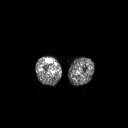
FDG PET of an extremity soft-tissue mass (from a PET/CT study), one axial slice. Position 231 of 311 along the scan axis. 128 × 128 image matrix, field of view 700 × 700 mm. Patient: male, 56 years. From the clinical record (not read from this slice): histological type: pleiomorphic leiomyosarcoma; grade: intermediate; site of the primary tumour: right thigh.
Outlined on this slice (expert contour drawn on MRI and transferred to this co-registered scan by the dataset authors):
- gross tumour volume including surrounding oedema: bounding box <46,59,51,62> (left, top, right, bottom; pixels)